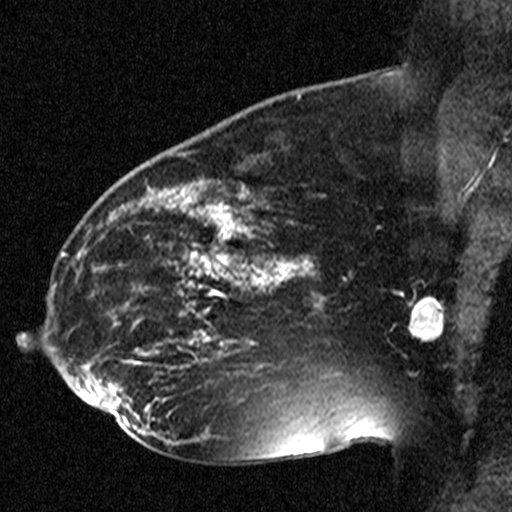
Breast MRI (dynamic contrast-enhanced), one sagittal slice; position 28 of 44 along the scan axis; dynamic contrast-enhanced study with each time point stored as its own series, time point 2 of 3 at this slice position (early post-contrast, ordered by acquisition time); 1.5 T; TE 4.5 ms, TR 11 ms; 512 × 512 image matrix, field of view 200 × 200 mm. Female patient, age 38 years. From the clinical record (not read from this slice): setting: breast cancer imaged before/during neoadjuvant chemotherapy; receptor status: HR-positive, HER2-negative.
Outlined on this slice (semi-automatic segmentation, software-assisted and operator-edited):
- analysis volume of interest (the breast-tissue region the enhancement analysis was run in; not a lesion): bounding box (x1, y1, x2, y2) in pixels: (176, 272, 251, 349)
- tumour enhancement mask (voxels above the 90 % enhancement threshold inside the analysis volume of interest): (180, 272, 250, 345)